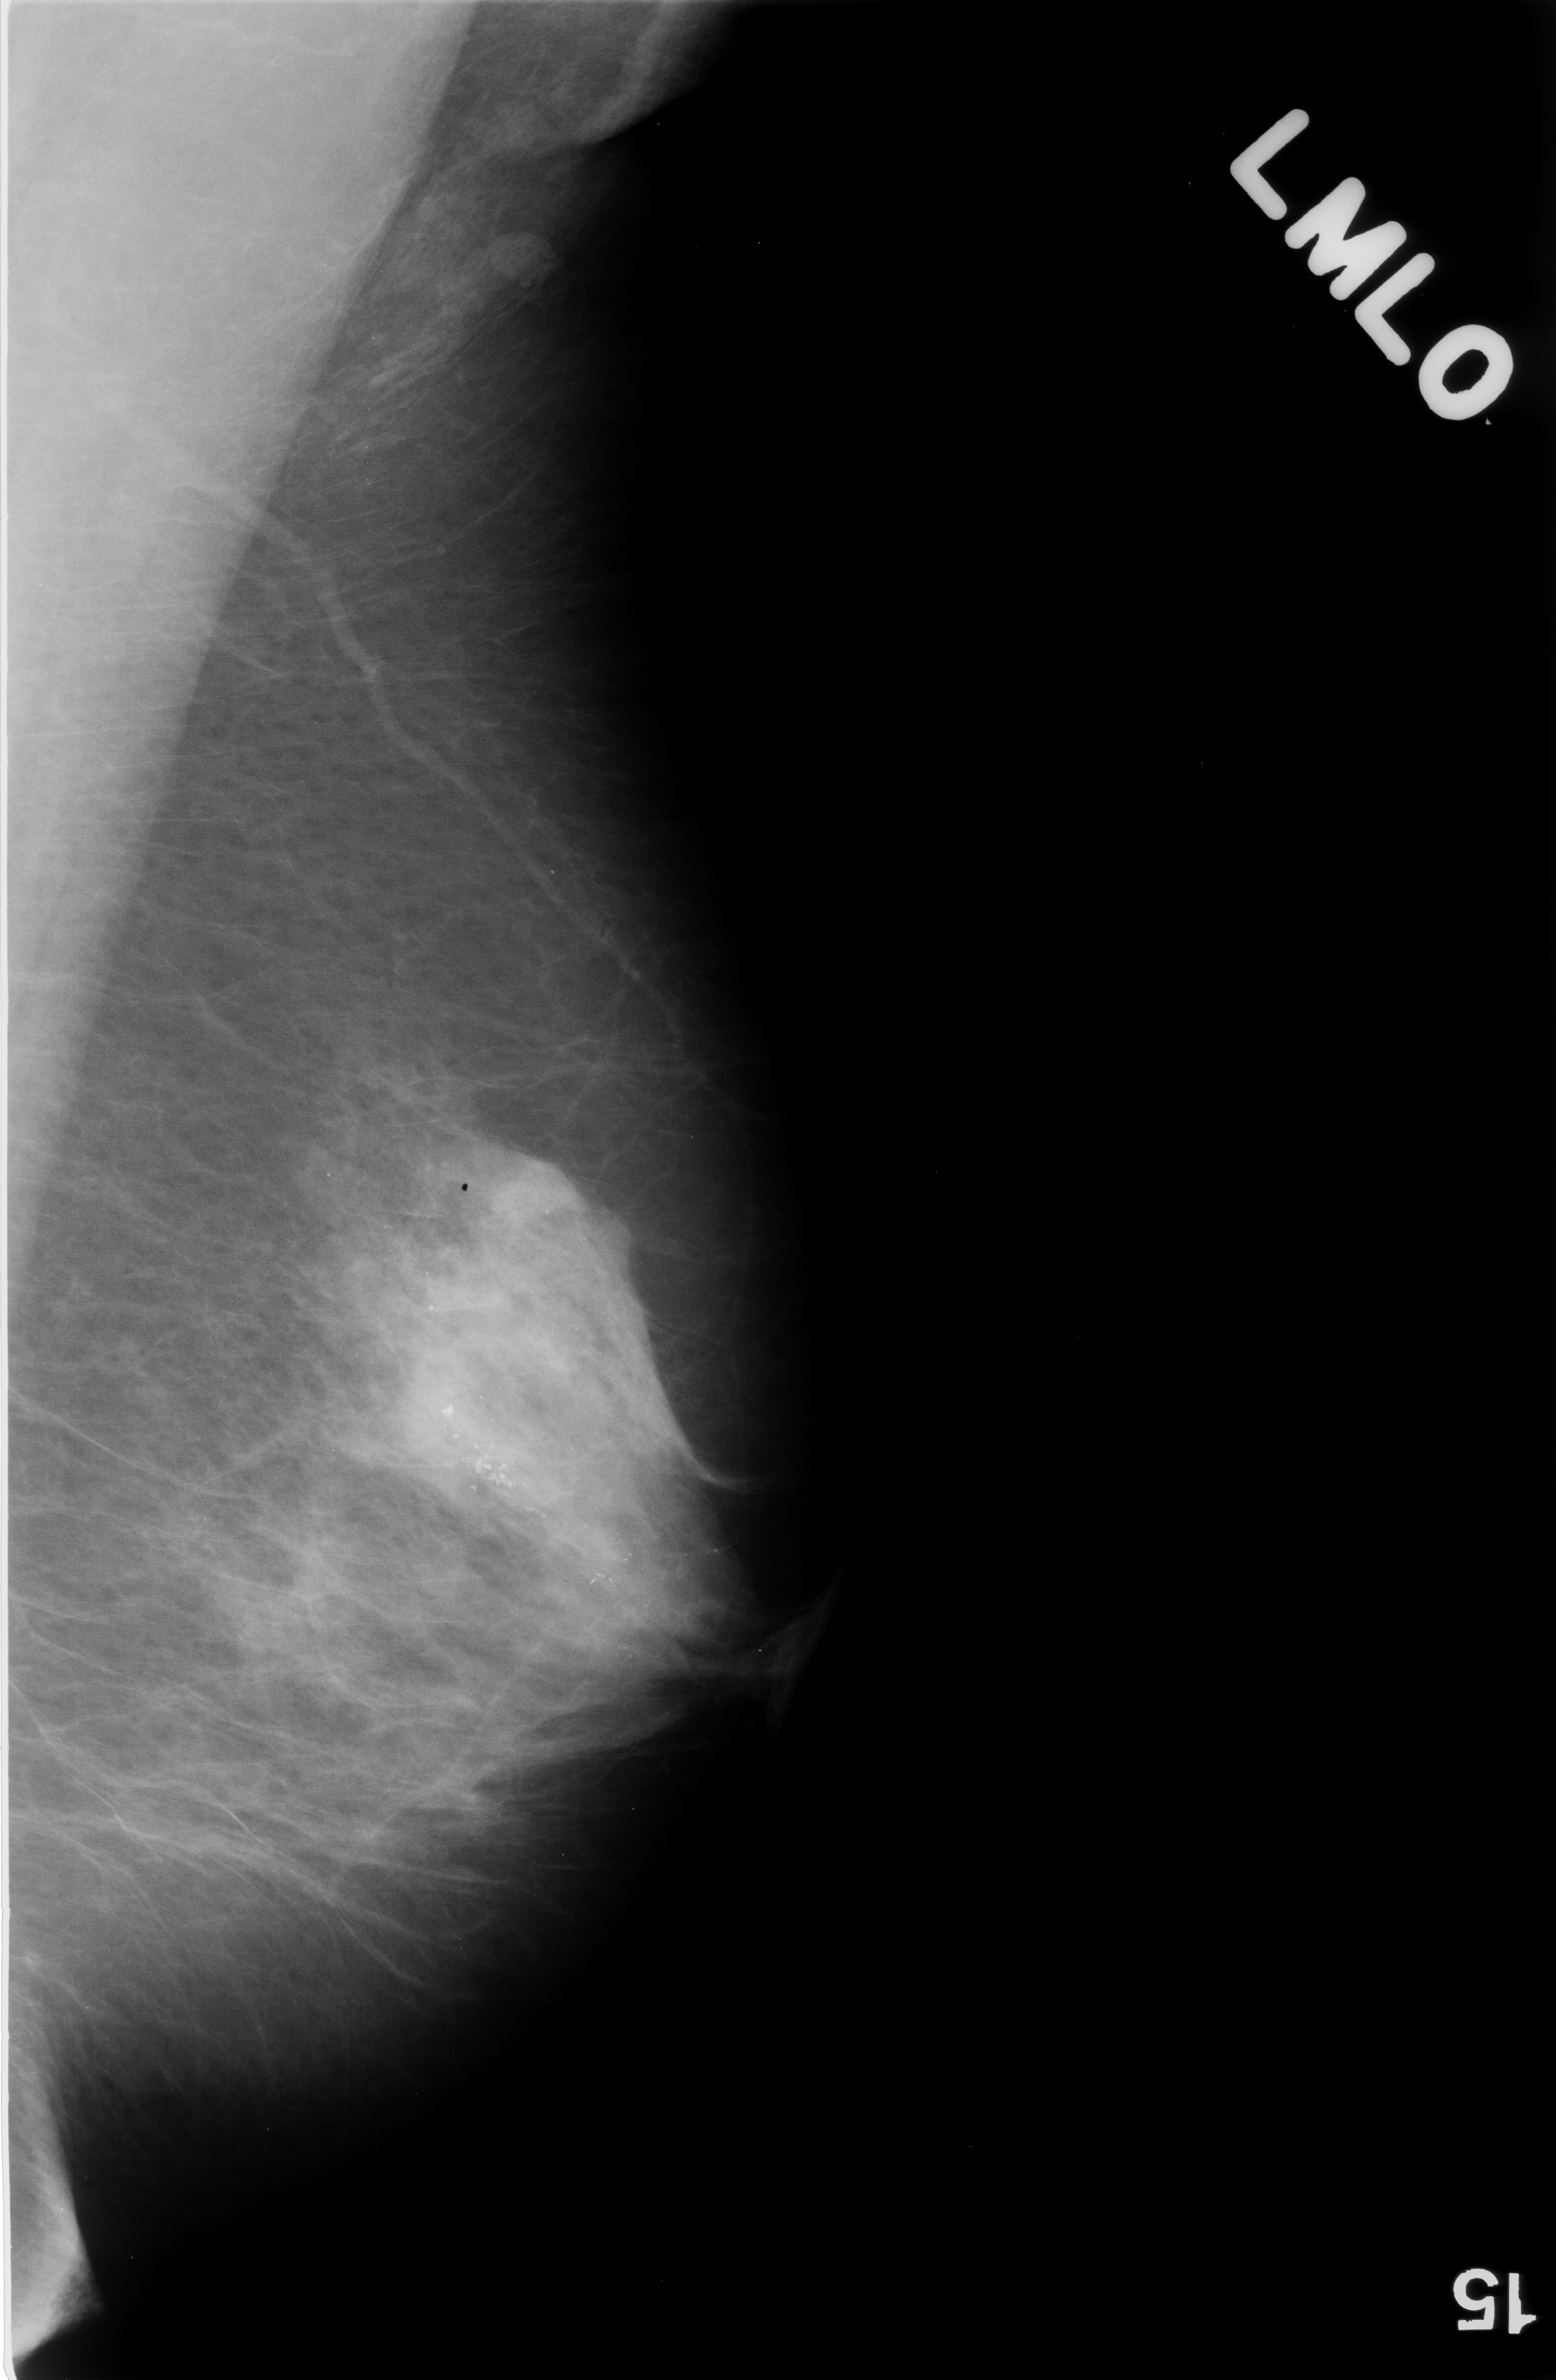
Mammogram (digitized film); left breast; mediolateral oblique (MLO) view; breast composition: heterogeneously dense (BI-RADS density category 3 of 4); 1556 × 2380 image matrix.
Expert-marked regions of interest on this image (one box per marked abnormality):
- calcifications, morphology pleomorphic, distribution segmental; BI-RADS assessment category 5; pathology result (as recorded, not read from the image): malignant: bounding box [x1, y1, x2, y2] px = [330, 1133, 733, 1687]